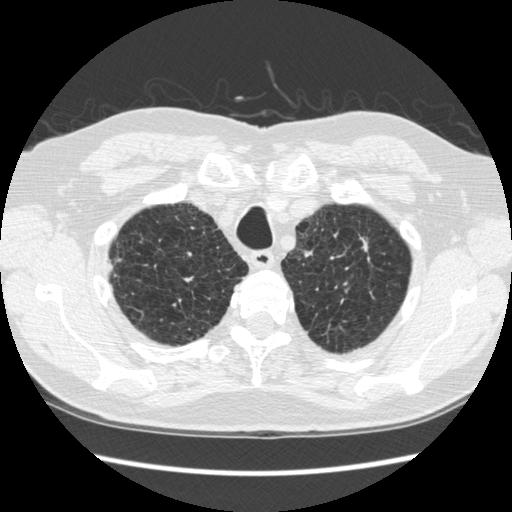
Axial slice from a low-dose chest CT screening exam. Second annual screen. Lung window (W 1500 / L -600 HU). 1.25 mm slice thickness. 120 kVp. Male, age 70 years at enrolment. Former smoker at enrolment.
Lesion marked by an expert reader, bounding box <330,220,391,288> (left, top, right, bottom; pixels). The screening reader recorded 5 non-calcified nodules or masses ≥4 mm on this exam (right lower lobe, right lower lobe, right lower lobe, left upper lobe, left lower lobe); which of them this box marks is not recorded. Official screen result: positive, change unspecified: nodule(s) >= 4 mm or enlarging nodule(s), mass(es), or other non-specific abnormalities suspicious for lung cancer. Later outcome: lung cancer diagnosed 479 days after this screen (after the third annual screen) — squamous cell carcinoma, NOS, left upper lobe, moderately differentiated (G2), stage IA (AJCC 6th edition), 18 mm at pathology.